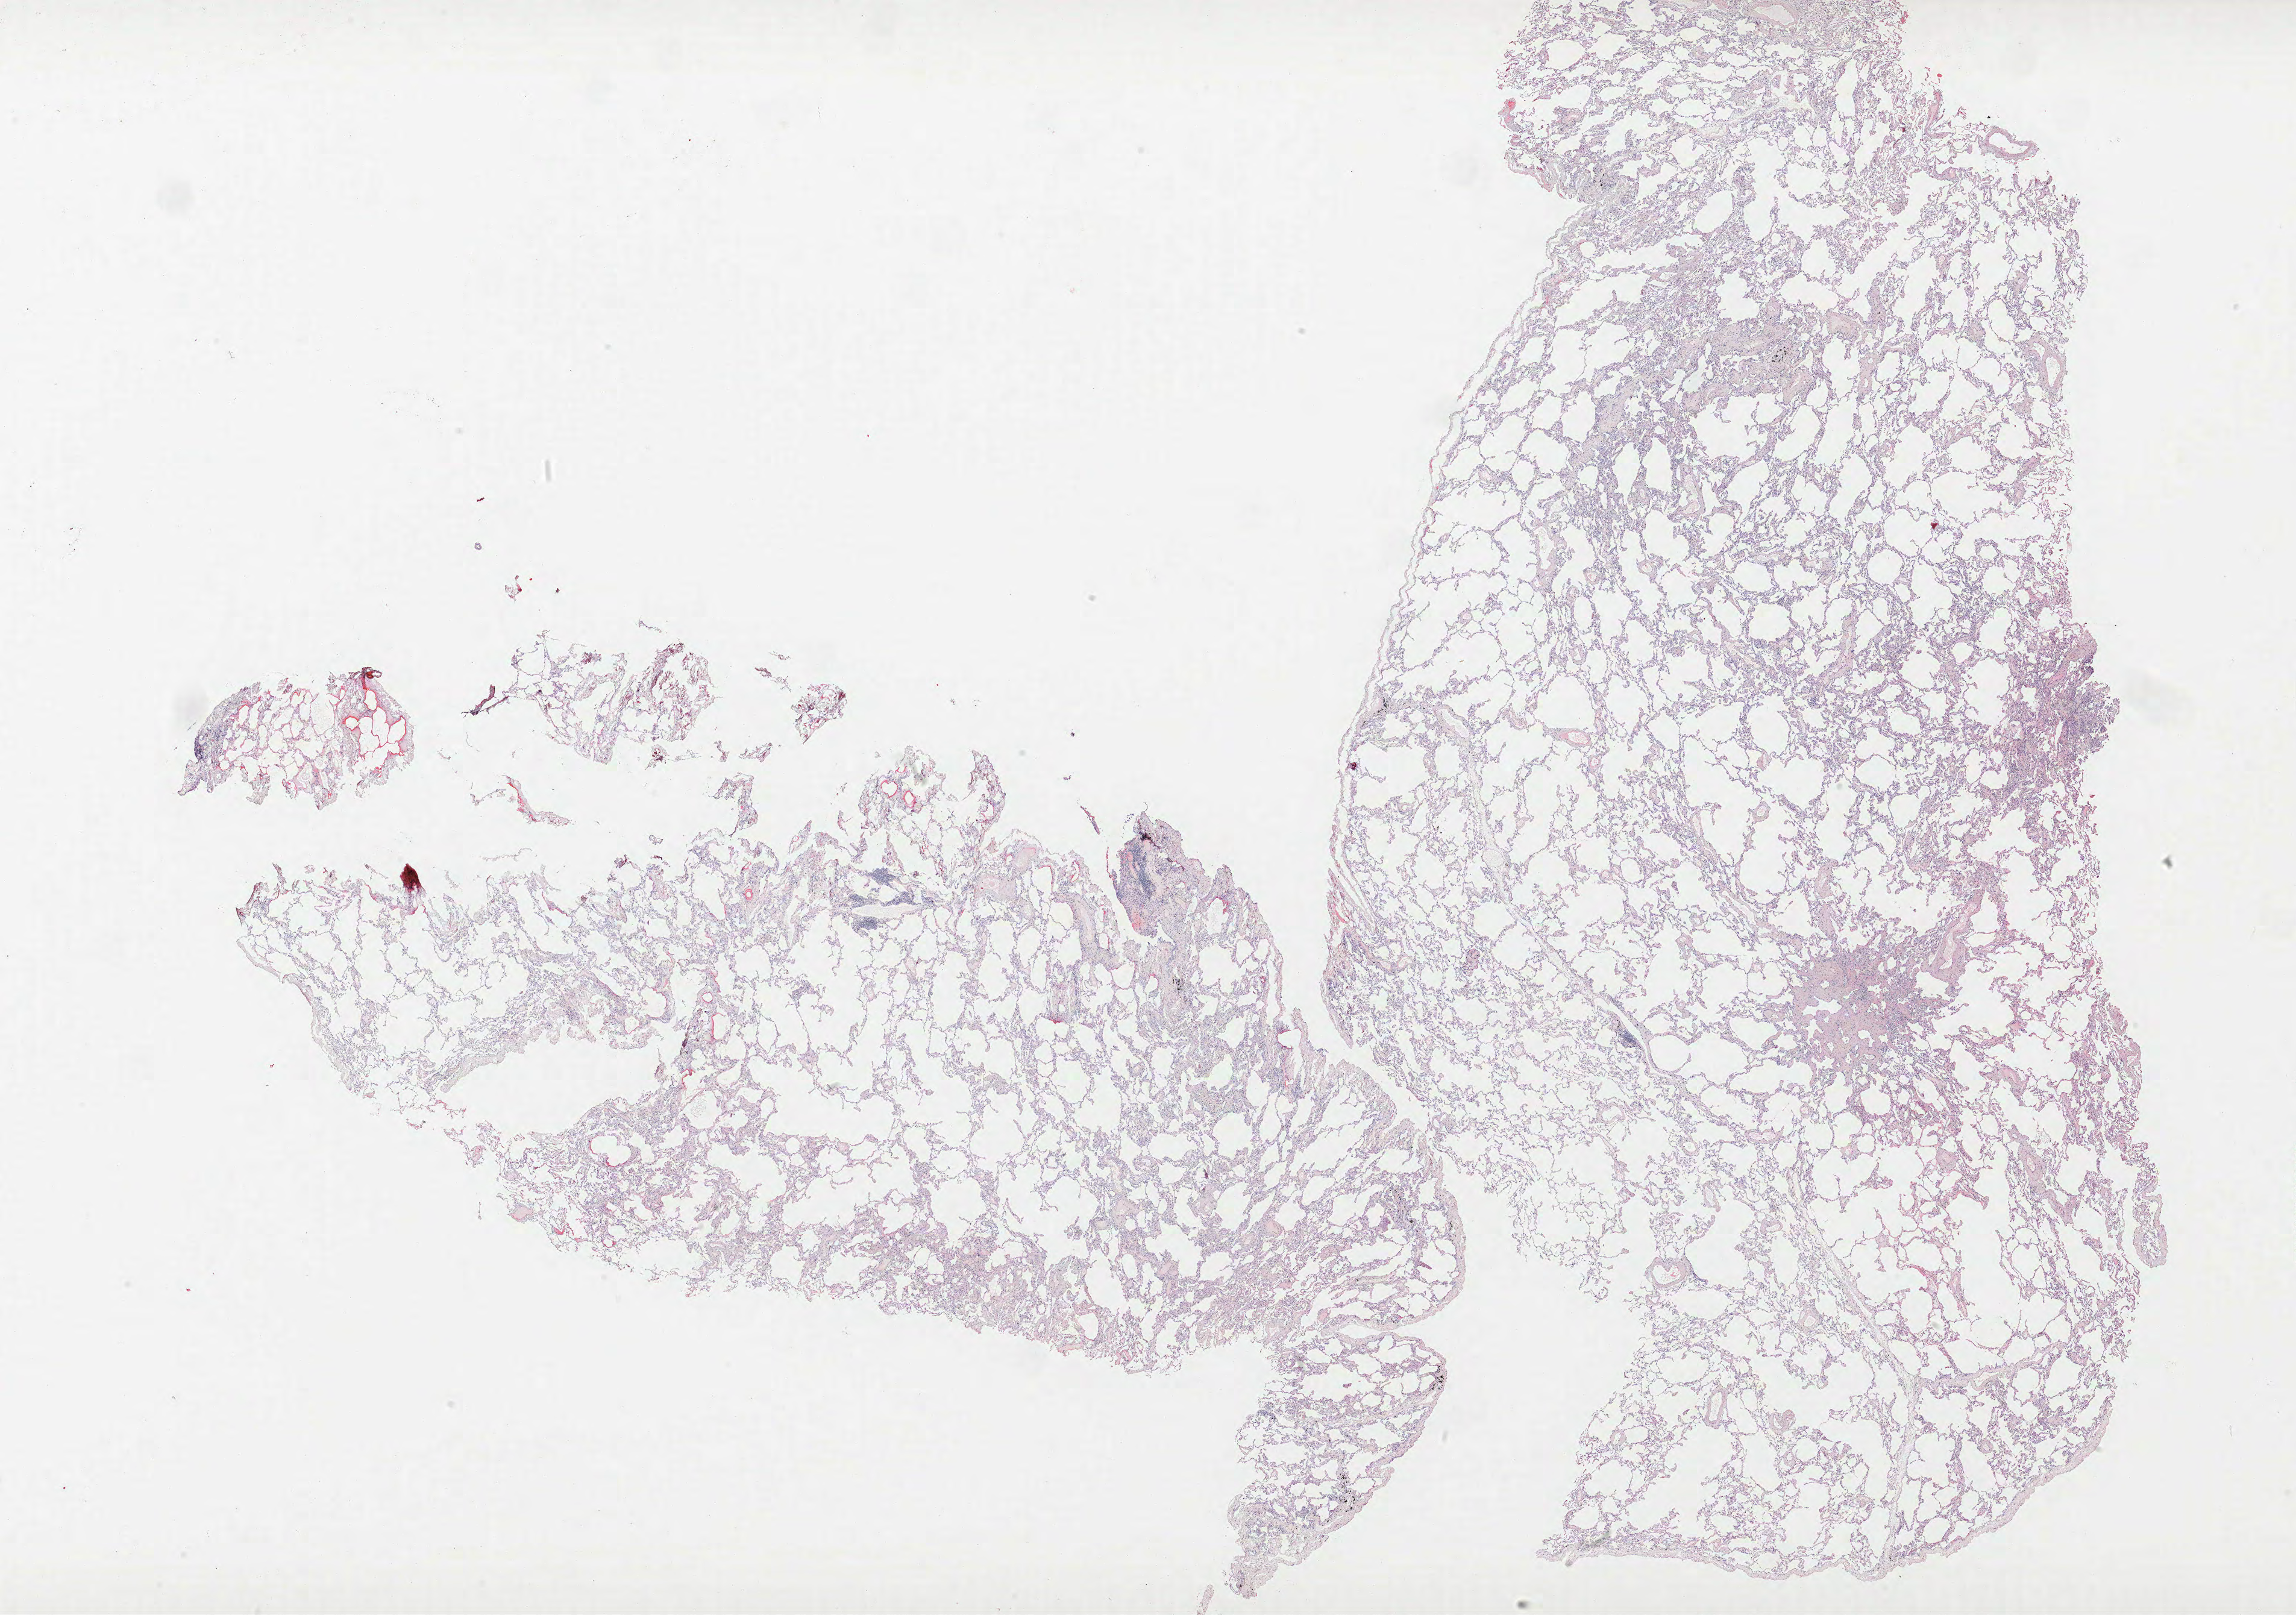
H&E-stained whole-slide image, a low-resolution overview of the entire scanned area, about 30.5 x 21.4 mm (from a 40x scan). Formalin-fixed paraffin-embedded (FFPE) section. Lung. Male, age 64 at enrolment. Former smoker at enrolment.
Participant's lung-cancer diagnosis: Bronchiolo-alveolar adenocarcinoma, NOS. Note: participant had 2 primary lung cancers recorded; fields above describe the first.